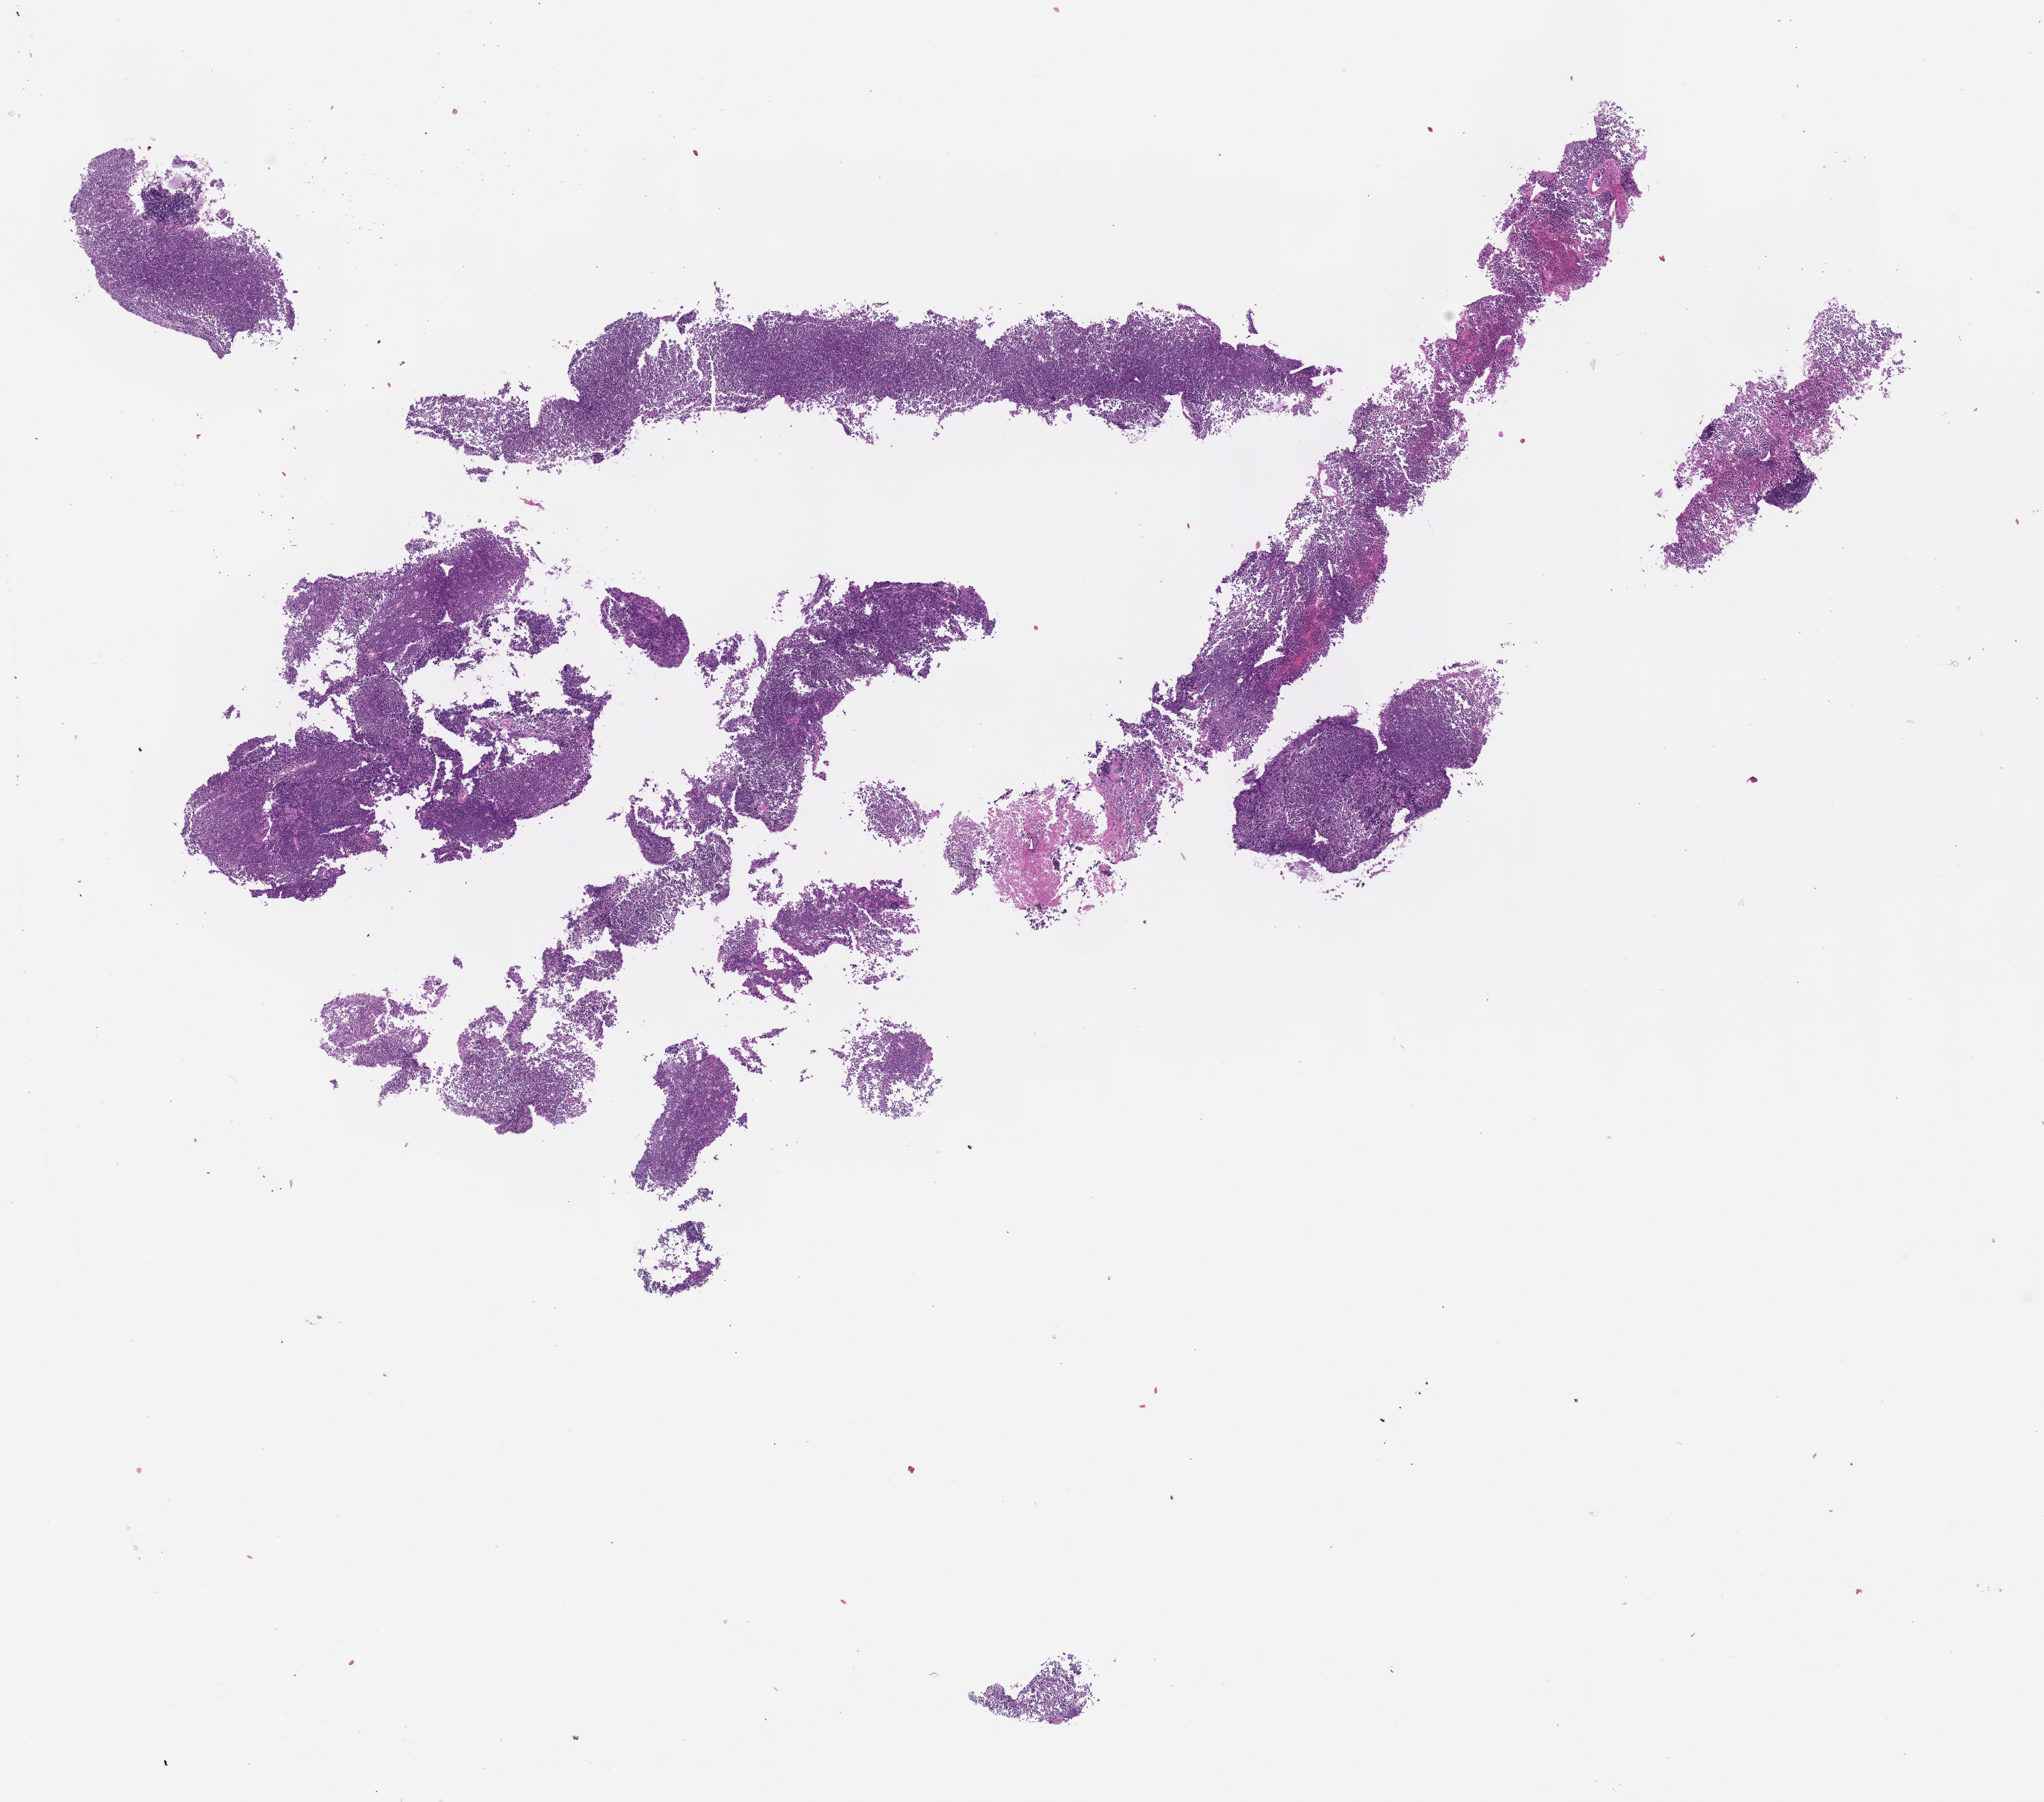
H&E whole-slide image, a low-resolution overview of the entire scanned area, about 12.1 x 10.6 mm; tumor tissue; anatomic site: kidney. Male patient; age at initial diagnosis 3 years.
Diagnosis: Burkitt lymphoma, NOS.